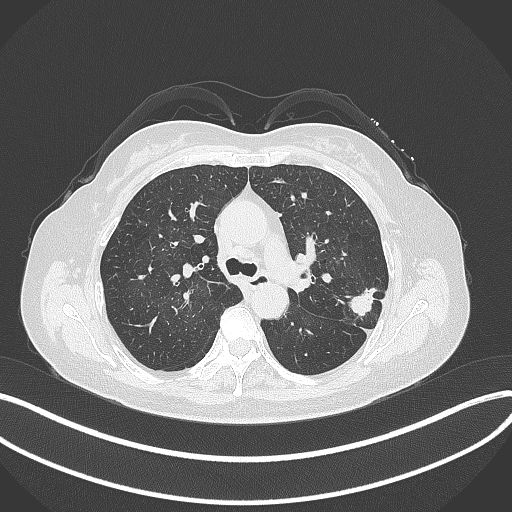
Chest CT, one axial slice. Position 213 of 319 along the scan axis. Reconstruction kernel B70f. Lung window (W 1500 / L -600 HU). 512 × 512 image matrix. Female patient, age 60 years. From the clinical record (not read from this slice): clinical TNM (as recorded): T1c N0 M0.
Outlined on this slice (rectangle marked by the reading radiologist):
- lung tumour (recorded histology: adenocarcinoma): bounding box (x1, y1, x2, y2) in pixels: (344, 278, 377, 325)